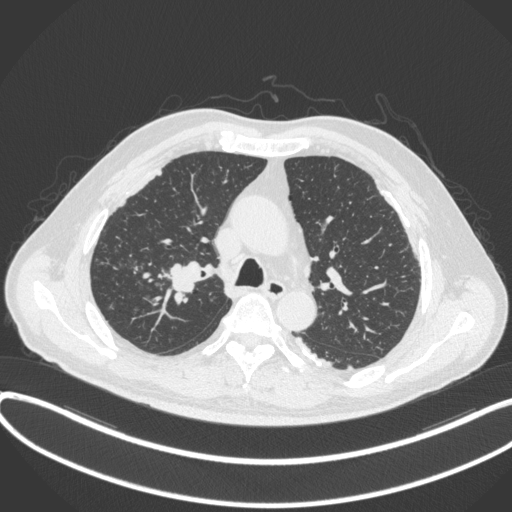
Chest CT, one axial slice; position 290 of 455 along the scan axis; reconstruction kernel B31f; lung window (W 1500 / L -600 HU); 1 mm slice thickness; 512 × 512 image matrix, field of view 400 × 400 mm. Patient: male, 58 years. From the clinical record (not read from this slice): clinical TNM (as recorded): T1c N0 M0.
Outlined on this slice (bounding box drawn by a radiologist):
- lung tumour (recorded histology: squamous cell carcinoma): bounding box <167,260,207,297> (left, top, right, bottom; pixels)